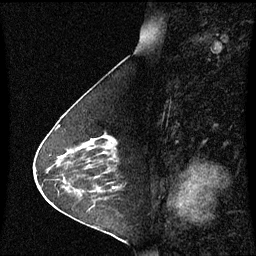
Breast MRI (dynamic contrast-enhanced), one sagittal slice. Slice 27 of 60 in the series (ordered by position). Dynamic contrast-enhanced series, image 2 of 3 at this slice position (ordered by acquisition). 1.5 T. TE 4.2 ms, TR 8.9 ms. 2 mm slice thickness. 256 × 256 image matrix. Female patient, age 63 years. Case-level facts recorded for this patient, not image findings: setting: breast cancer imaged before/during neoadjuvant chemotherapy; receptor status: HR-positive, HER2-negative.
Annotated regions visible in this slice (semi-automatically segmented with operator editing):
- analysis volume of interest (the breast-tissue region the enhancement analysis was run in; not a lesion): bounding box <76,135,120,178> (left, top, right, bottom; pixels)
- tumour enhancement mask (voxels above the 70 % enhancement threshold inside the analysis volume of interest): <106,136,115,143>